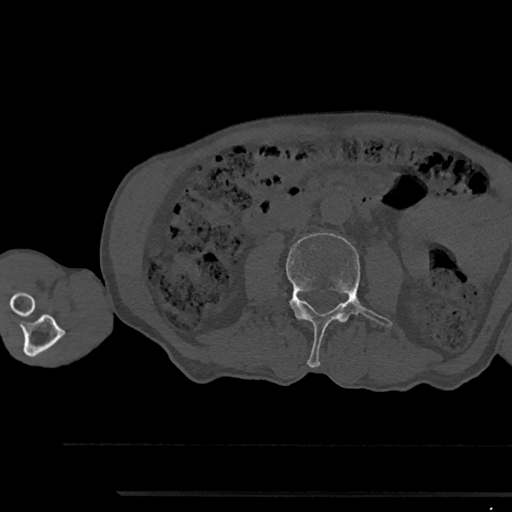
CT including the spine, one axial slice. Position 487 of 797 along the scan axis. Reconstruction kernel Br40s/3. Bone window (W 1800 / L 400 HU). 0.5 mm slice thickness. 512 × 512 image matrix, field of view 367 × 367 mm. Male patient, age 79 years. From the clinical record (not read from this slice): primary cancer: prostate.
Outlined on this slice (semi-automatic segmentation, software-assisted and operator-edited):
- L3 vertebra: bounding box <286,233,392,367> (left, top, right, bottom; pixels)